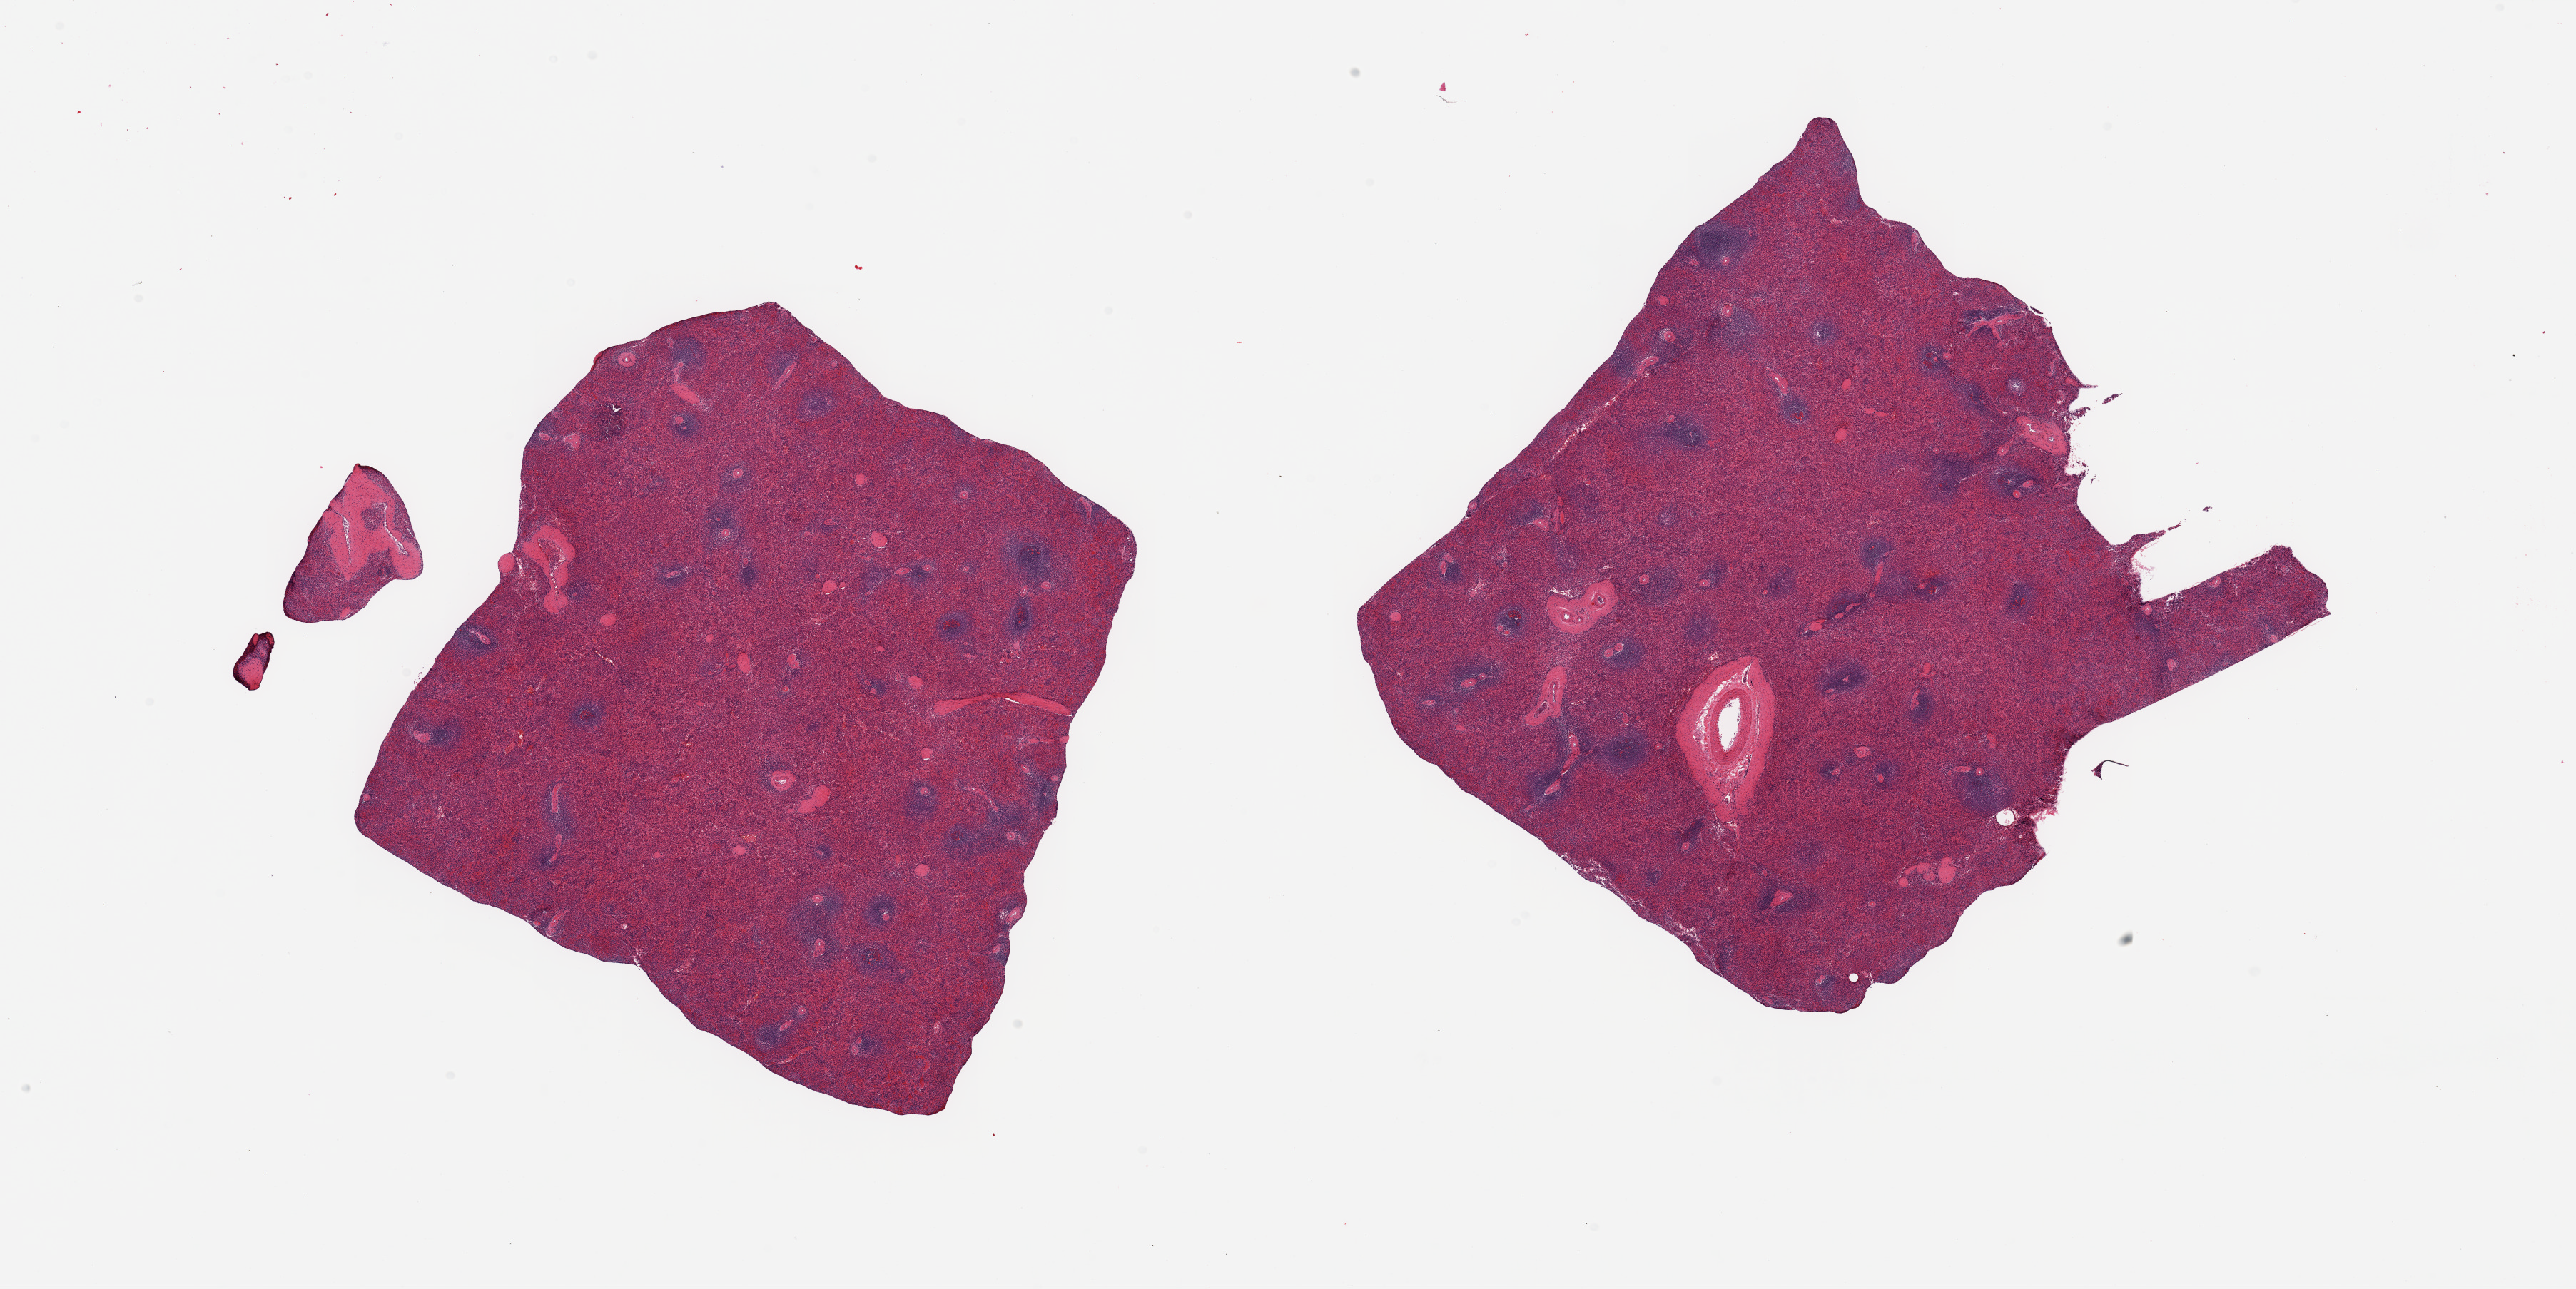
Whole-slide image, haematoxylin and eosin stain, shown as a low-resolution overview of the whole scanned area (about 28.5 x 14.3 mm), PAXgene-fixed, paraffin-embedded tissue, sampled site (target tissue): spleen, tissue donor sample. Donor sex: male.
* review note (as recorded): 2 pieces